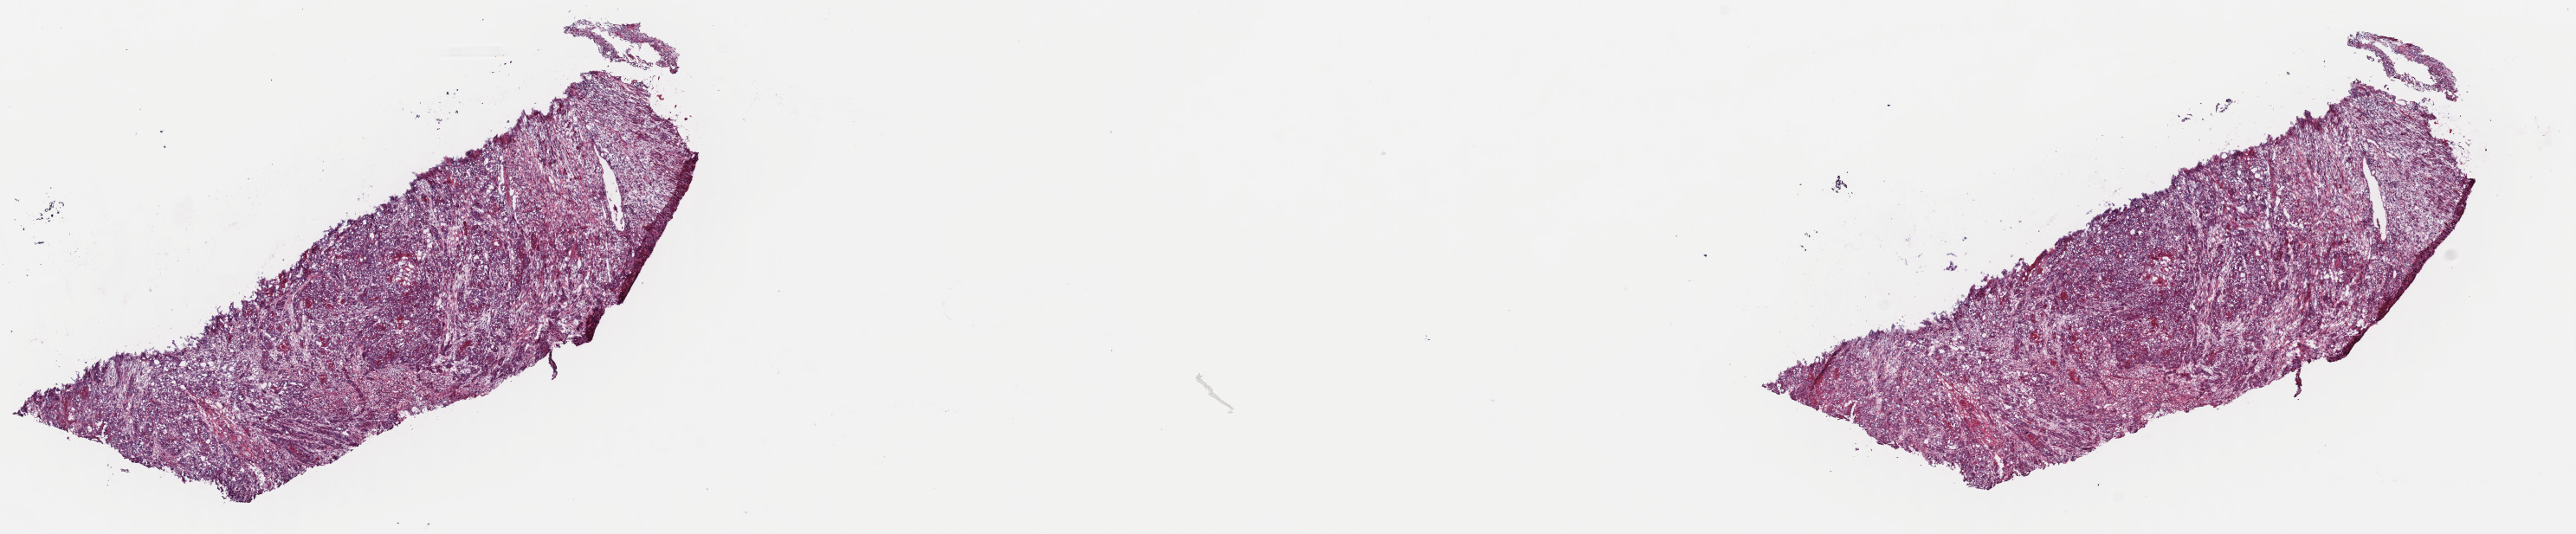
H&E-stained whole-slide image — low-resolution overview of the scanned area, about 23.5 x 4.9 mm; frozen section; sample: primary tumour, head and neck. Female, age 70 years at initial diagnosis.
Histologic diagnosis: Squamous cell carcinoma, keratinizing, NOS (tongue, NOS).